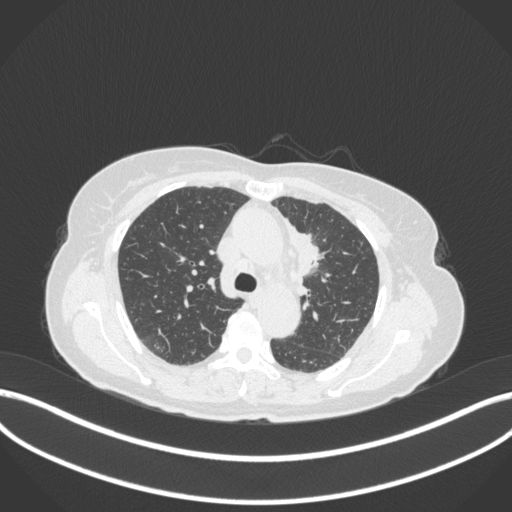
Chest CT, one axial slice; position 230 of 368 along the scan axis; 120 kVp; lung window (W 1500 / L -600 HU); 1 mm slice thickness; 512 × 512 image matrix. Patient: female, 65 years. Case-level facts recorded for this patient, not image findings: clinical TNM (as recorded): T2a N0 M0; histopathological grade: G2-3.
Annotated regions visible in this slice (rectangle marked by the reading radiologist):
- lung tumour (recorded histology: adenocarcinoma): box from (x=285, y=219) to (x=328, y=282) px